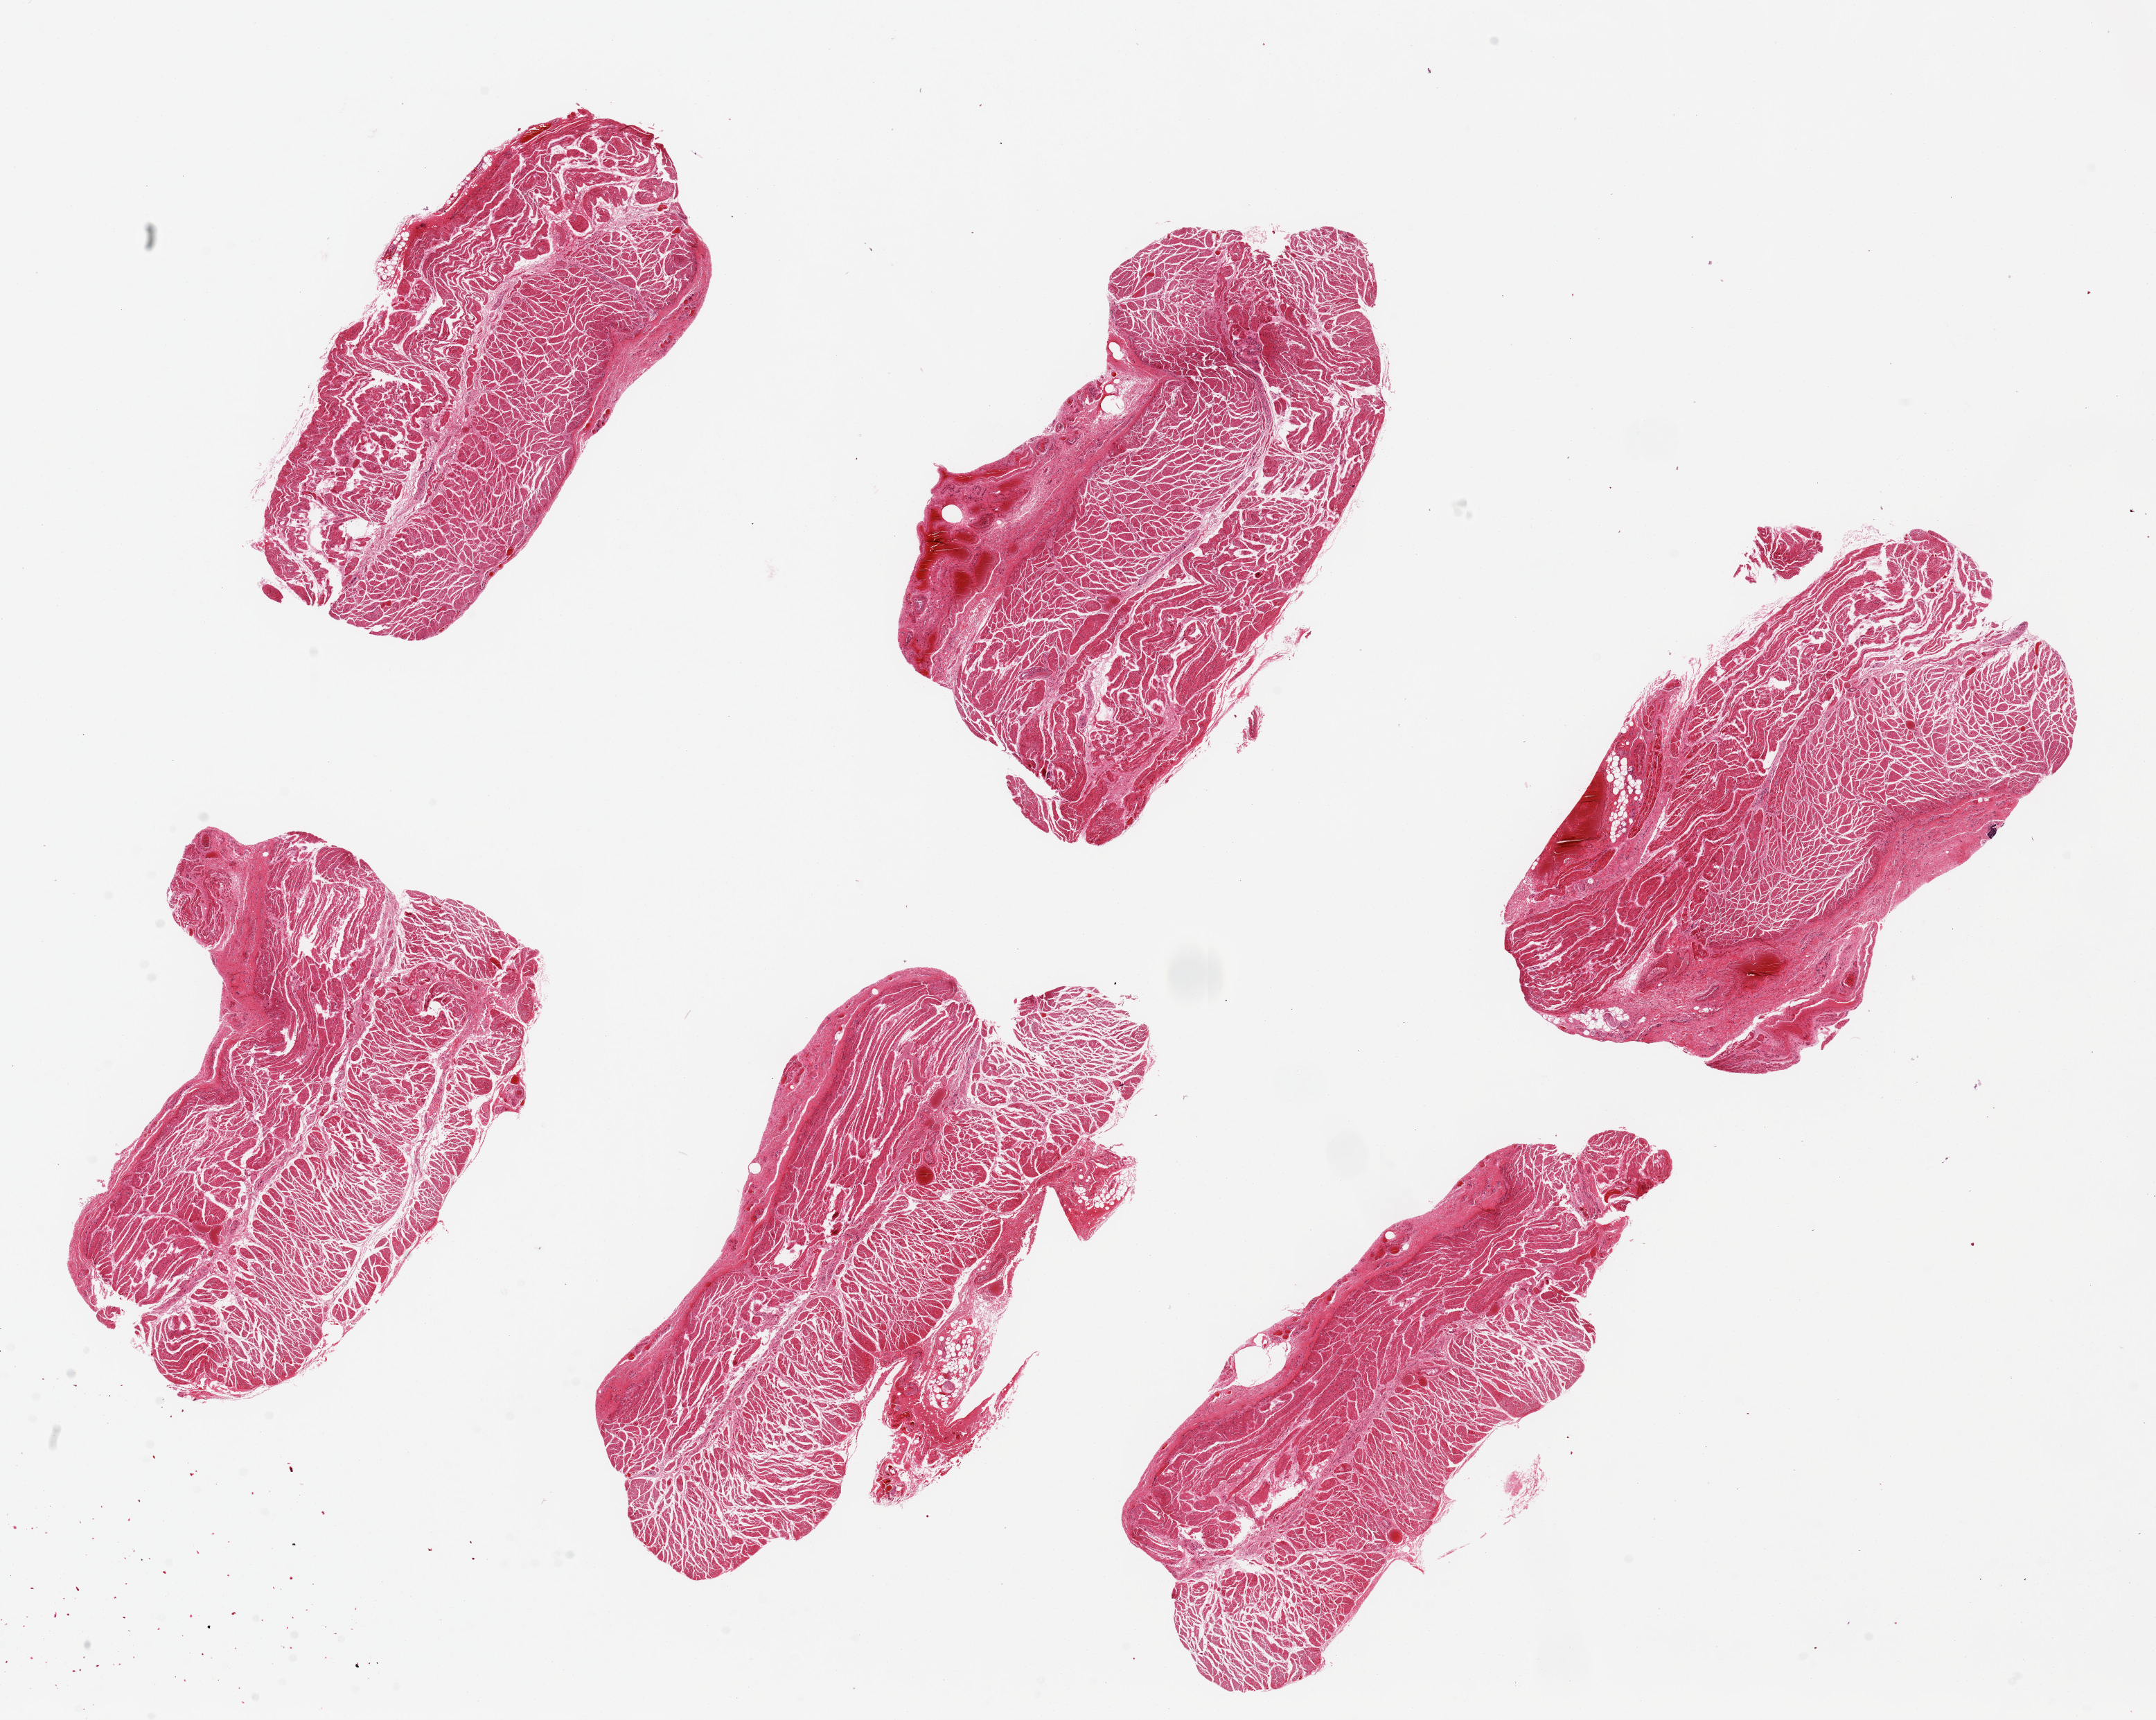
Whole-slide image, H&E stain — a low-resolution overview of the entire scanned area, about 24.6 x 19.6 mm (from a 20x scan), PAXgene-fixed paraffin-embedded (PFPE) section, sampled site (target tissue): esophageal muscle, tissue donor sample. Donor sex: male.
Reviewer comment on this tissue sample: 6 pieces ~8x3mm, all muscularis.